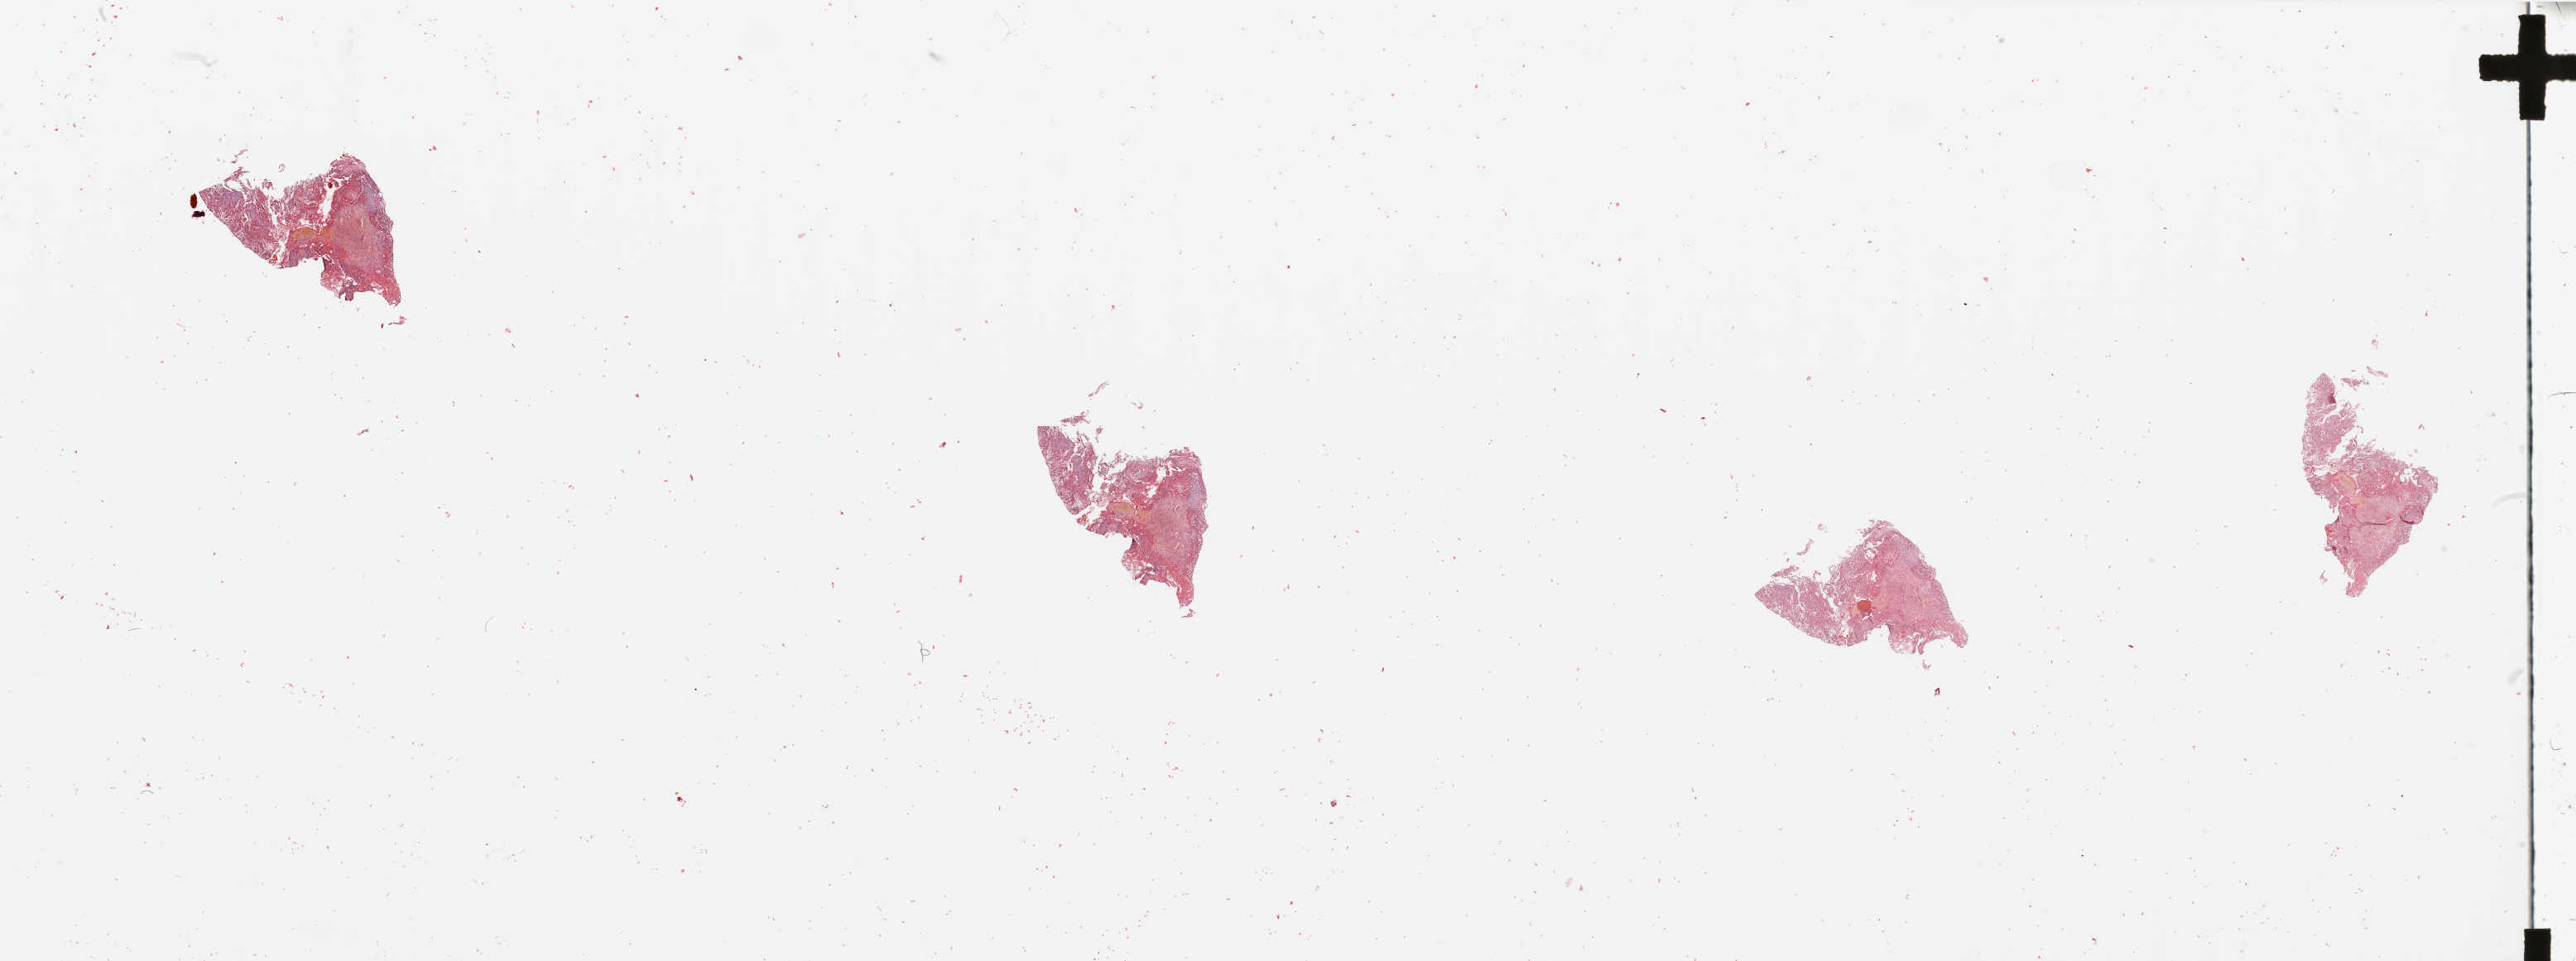
Digitized H&E tissue section (whole slide) — shown as a low-resolution overview of the whole scanned area (about 49.2 x 18.4 mm, acquisition: 20x scan). Tumour tissue sample, brain. Male, 62 y/o.
• diagnosis: Glioblastoma
• primary tumour site (as recorded): frontal lobe